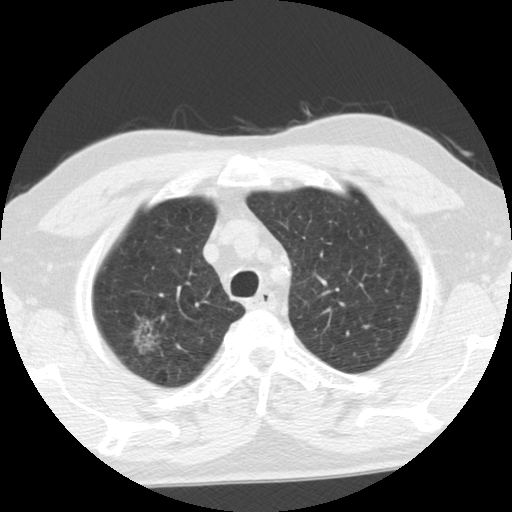
Low-dose screening chest CT, one axial slice. Reconstruction kernel STANDARD. Lung window (W 1500 / L -600 HU). 2.5 mm slice thickness. 512 × 512 image matrix.
Structures marked on this image (expert manual segmentation):
- lesion 1 (tumor, upper lobe of right lung): bounding box [x1, y1, x2, y2] px = [132, 312, 161, 355]